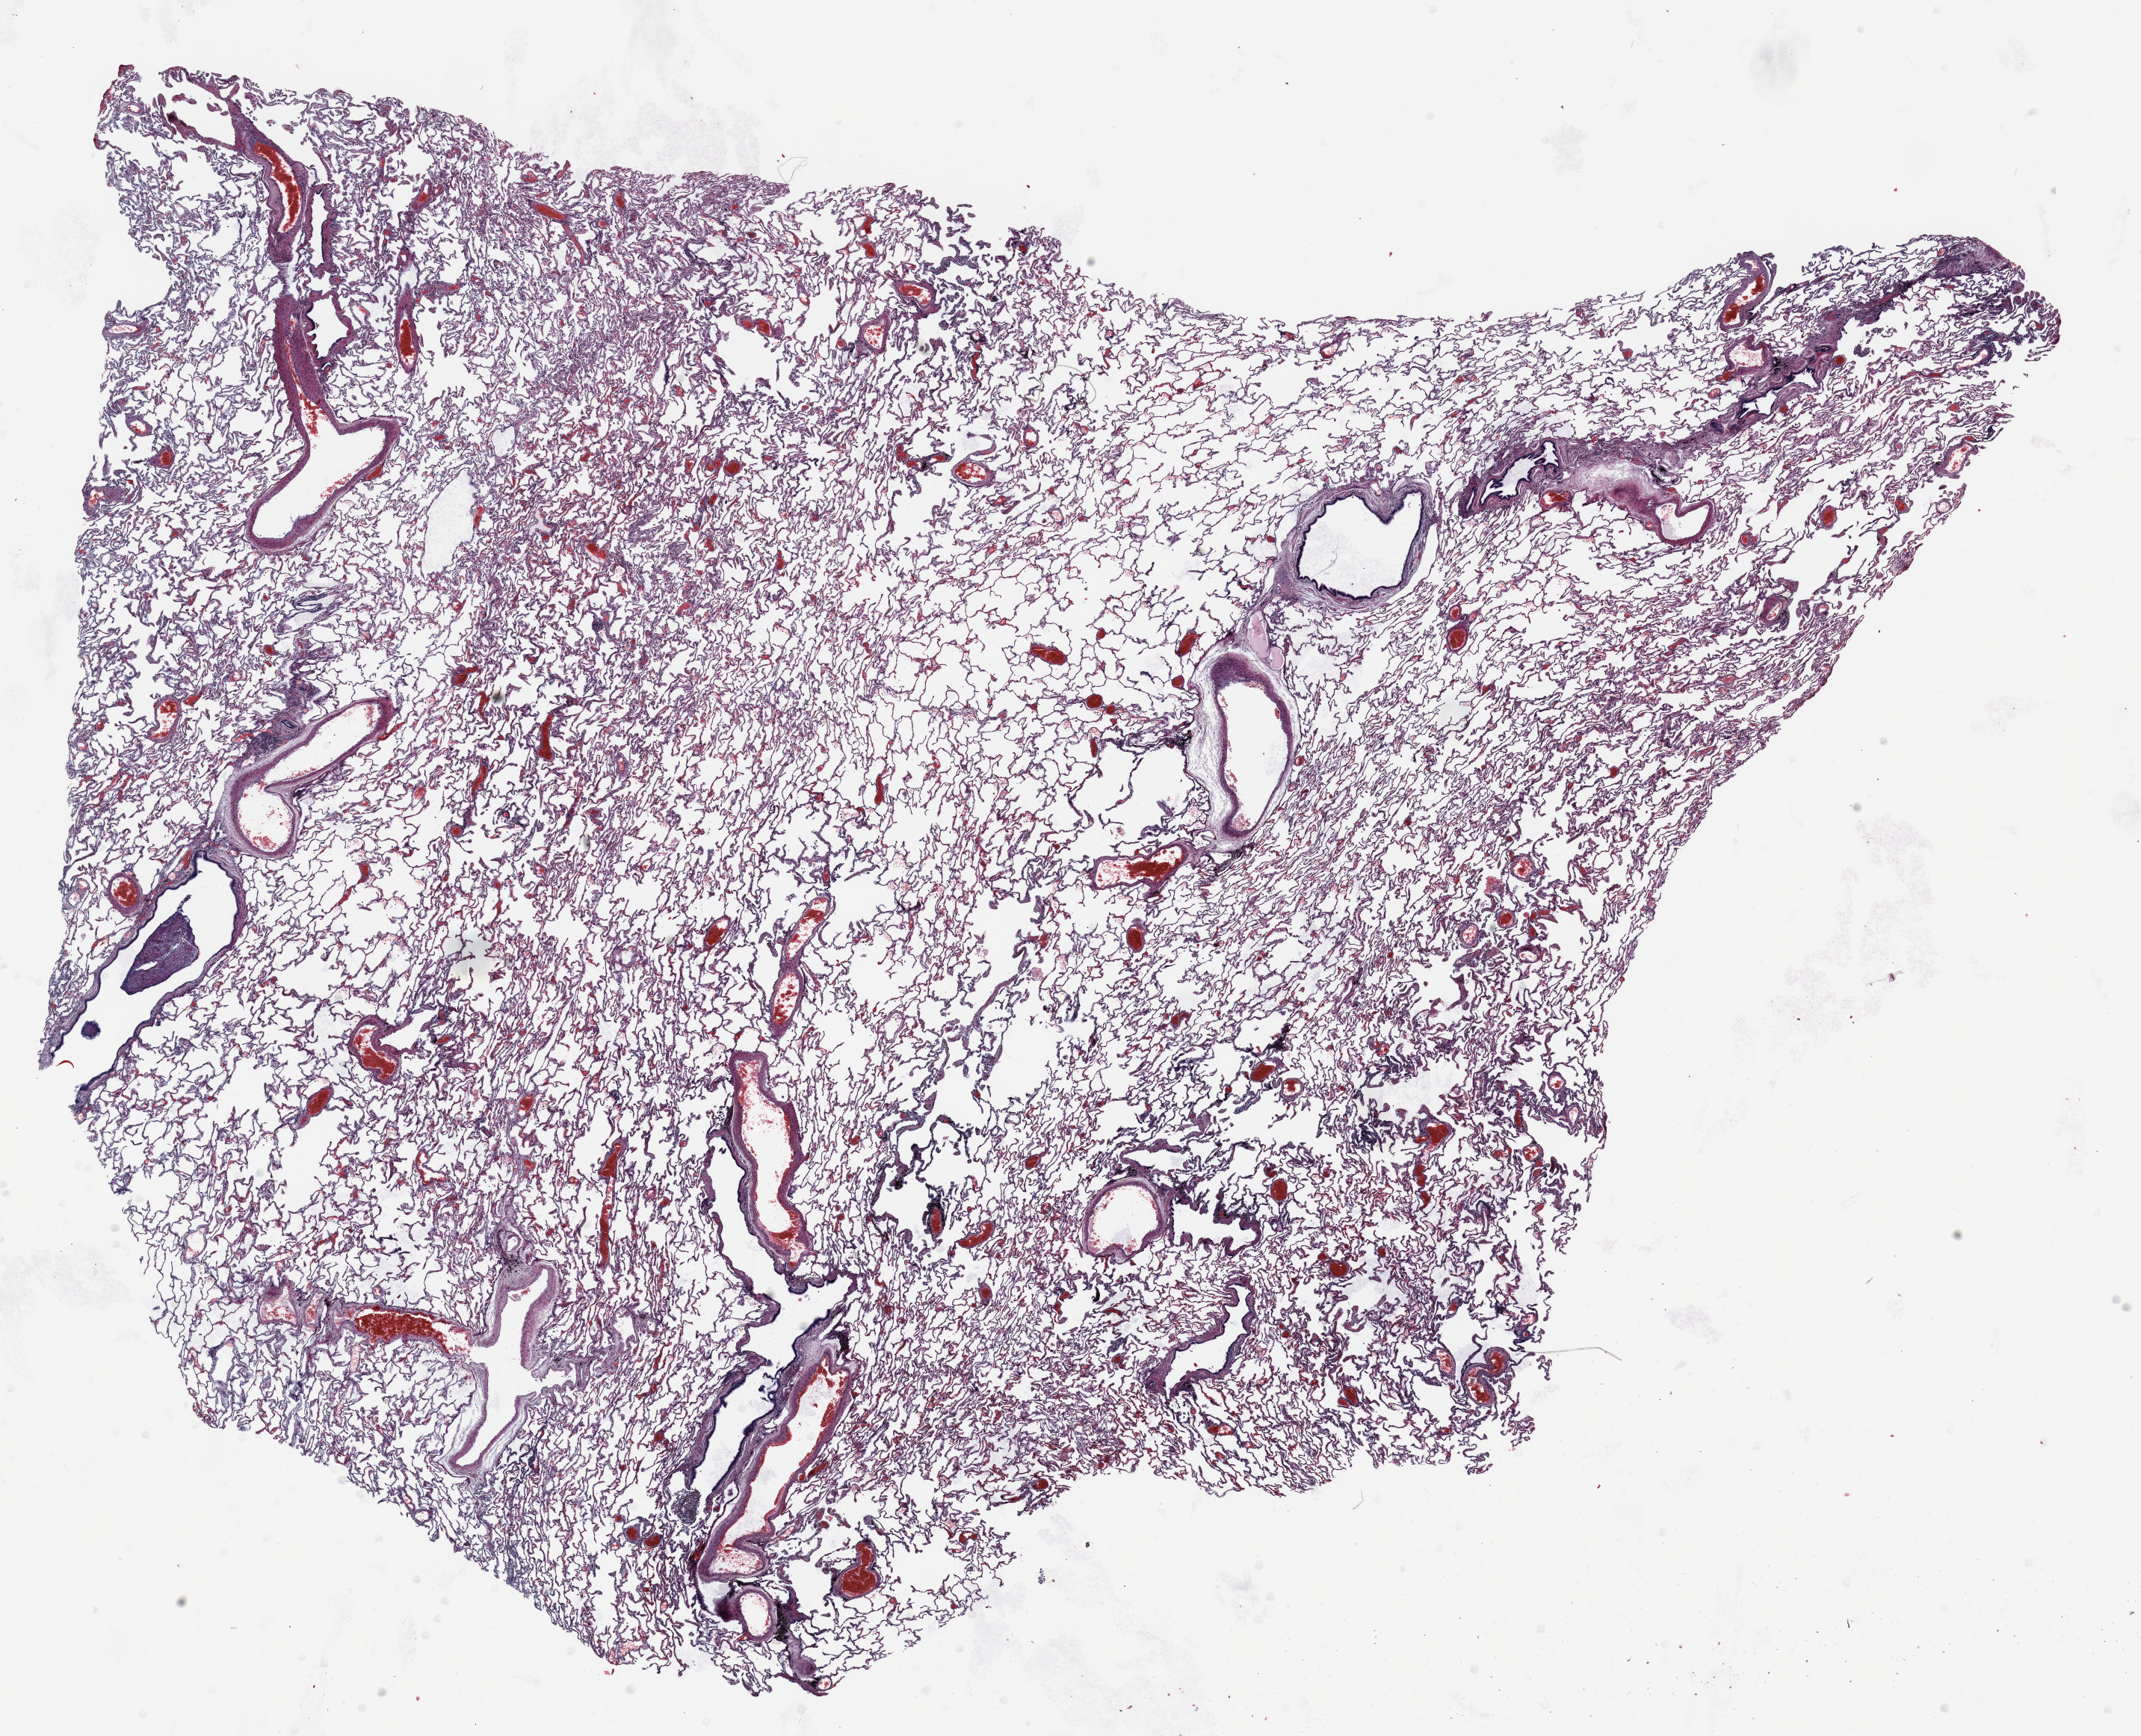
H&E-stained whole-slide image — whole scanned area (about 23.0 x 18.7 mm) shown as a low-resolution overview, FFPE section, lung tissue. Male patient, aged 67 at enrolment. Former smoker at enrolment. Grade: moderately differentiated (G2).
Participant's lung-cancer diagnosis: Atypical carcinoid tumor (ICD-O-3 8249/3). Tumour size (pathology): 10 mm. Primary tumour location (clinical record): left upper lobe. Stage (AJCC 6th edition): IA.